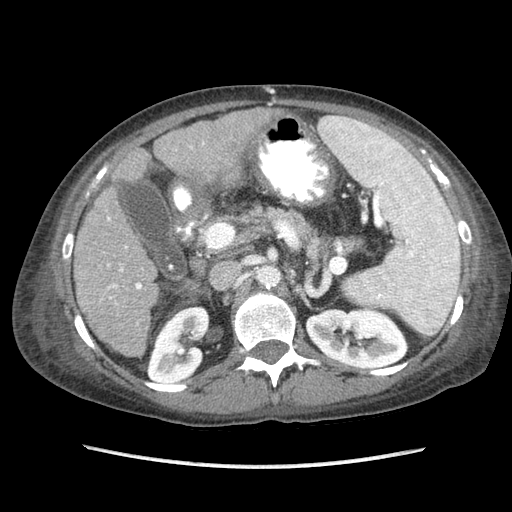
Contrast-enhanced abdominal CT (liver protocol), one axial slice. Position 39 of 87 along the scan axis. Reconstruction kernel STANDARD. Soft-tissue window (W 400 / L 40 HU). 2.5 mm slice thickness. 512 × 512 image matrix. From the clinical record (not read from this slice): diagnosis: hepatocellular carcinoma (patient treated with transarterial chemoembolisation; whether this scan precedes or follows treatment is not stated here); TNM stage (as recorded): Stage-IIIB; Child-Pugh class: A.
Annotated regions visible in this slice (semi-automatic segmentation, software-assisted and operator-edited):
- liver parenchyma outside the tumour (the mass and vessels are separate outlines, so this box may not span the whole liver): bounding box [x1, y1, x2, y2] px = [74, 108, 270, 356]
- liver vessels: [107, 142, 204, 299]